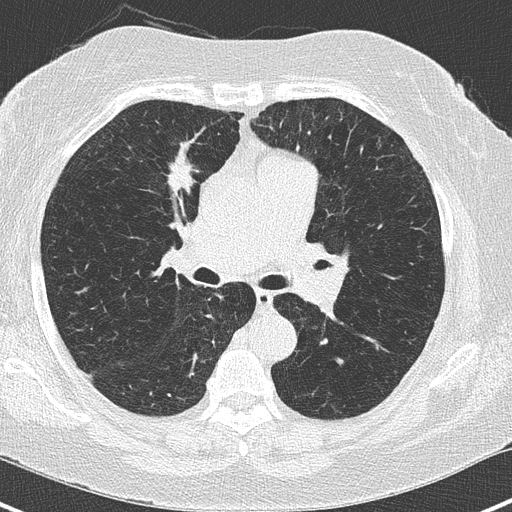
Axial slice from a low-dose chest CT screening exam. Third annual screen. Lung window (W 1500 / L -600 HU). 2 mm slice thickness. Lung (sharp) reconstruction kernel (B50f). 512 × 512 image matrix, field of view 303 × 303 mm. Female, age 62 years at enrolment. Current smoker at enrolment.
Expert reader's lesion annotation, bounding box <146,148,212,208> (left, top, right, bottom; pixels). The screening reader recorded 4 non-calcified nodules or masses ≥4 mm on this exam (right upper lobe, left lower lobe, left lower lobe); which of them this box marks is not recorded. Official screen result: positive, other. Later outcome: lung cancer diagnosed 41 days after this screen — adenocarcinoma, NOS, right upper lobe, moderately differentiated (G2), stage IA (AJCC 6th edition), 15 mm at pathology.